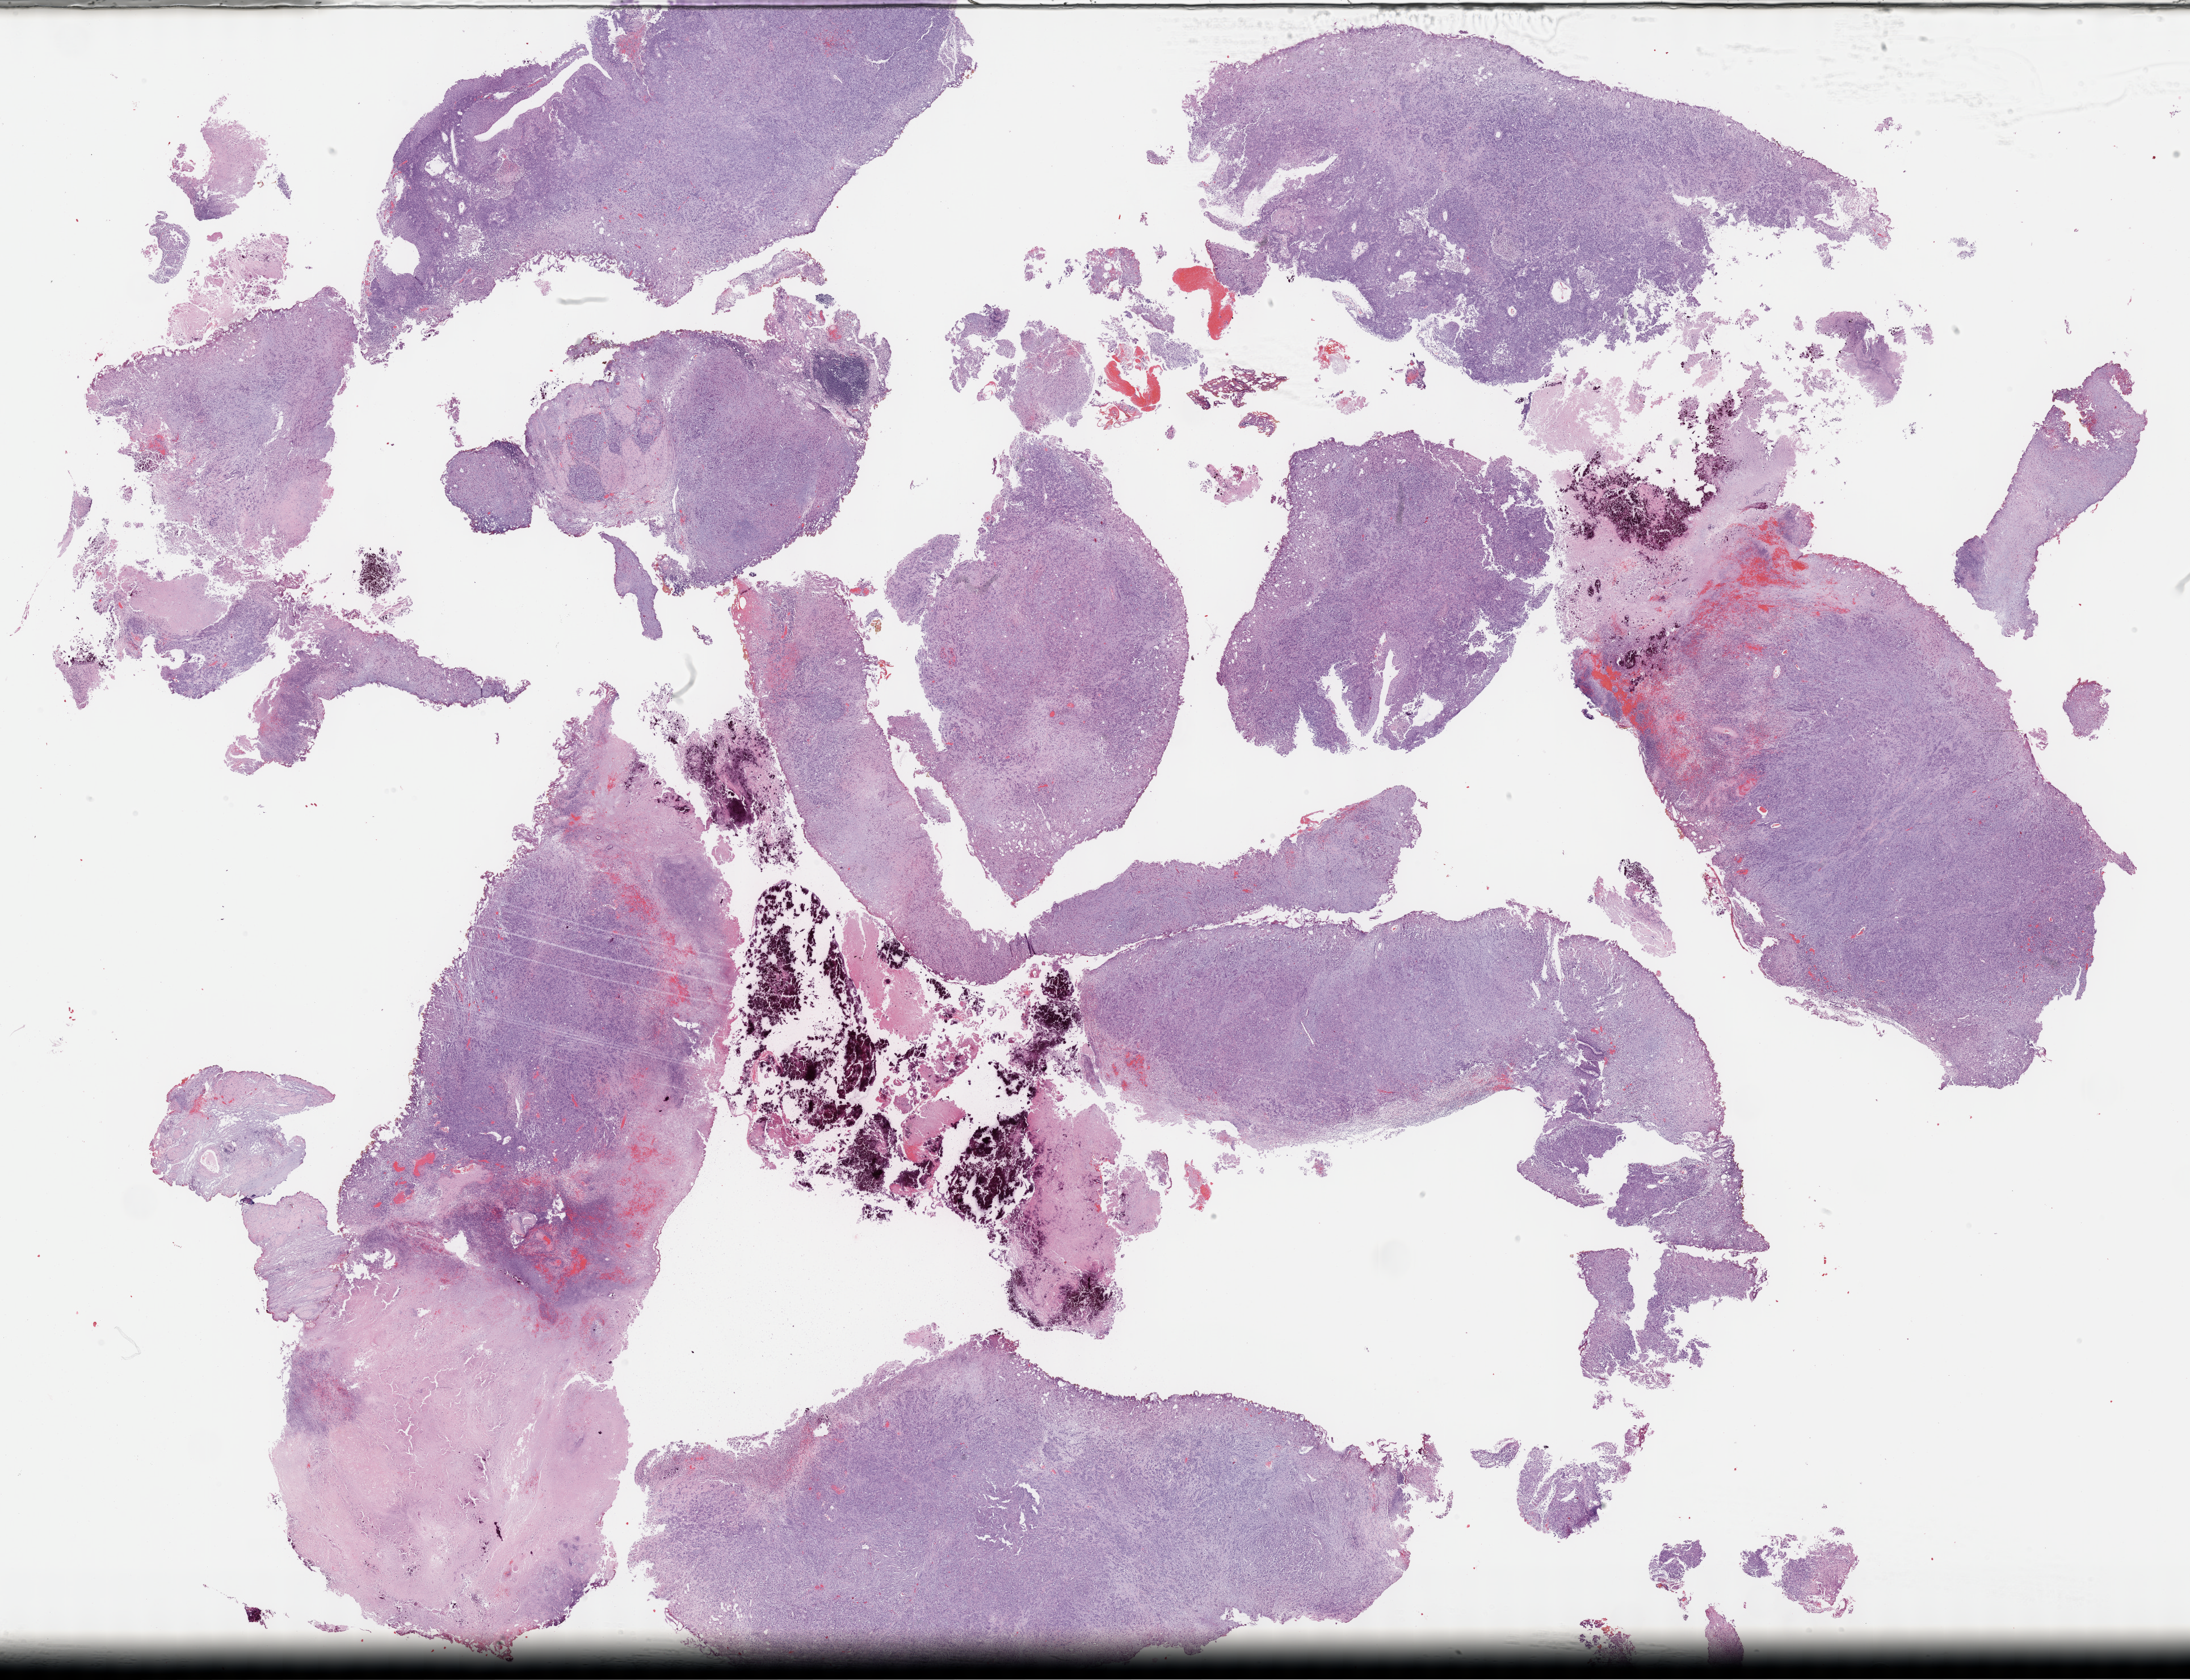
Digitized Hematoxylin and eosin (H&E) stained tissue section (whole slide), low-resolution overview of the scanned area, about 31.2 x 23.9 mm (from a 40x scan). FFPE section. Primary tumour sample from the bladder. Female, age 62 years at initial diagnosis. Histologic grade: high grade.
Diagnosis: Transitional cell carcinoma. TNM: T2 NX M1. AJCC pathologic stage: IV (7th edition).